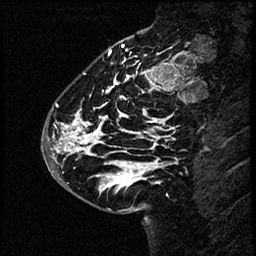
Breast MRI (dynamic contrast-enhanced), one sagittal slice; position 20 of 60 along the scan axis; dynamic contrast-enhanced study with each time point stored as its own series, time point 2 of 4 at this slice position (early post-contrast, ordered by acquisition time); 1.5 T; TE 4.2 ms, TR 17.6 ms; 2 mm slice thickness; 256 × 256 image matrix, field of view 200 × 200 mm. Female patient, age 43 years. Case-level facts recorded for this patient, not image findings: setting: breast cancer imaged before/during neoadjuvant chemotherapy.
Structures marked on this image (semi-automatically segmented with operator editing):
- analysis volume of interest (the breast-tissue region the enhancement analysis was run in; not a lesion): bounding box [x1, y1, x2, y2] px = [45, 57, 169, 191]
- tumour enhancement mask (voxels above the 100 % enhancement threshold inside the analysis volume of interest): [48, 71, 169, 190]